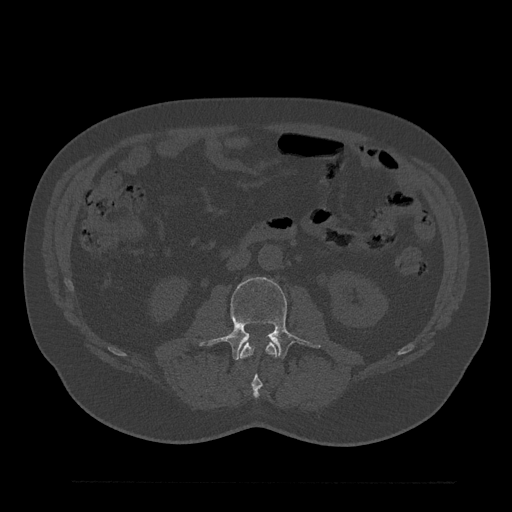
CT including the spine, one axial slice. Slice 54 of 797 in the series (ordered by position). Bone window (W 1800 / L 400 HU). 0.5 mm slice thickness. 512 × 512 image matrix, field of view 430 × 430 mm. Male patient, age 61 years. From the clinical record (not read from this slice): primary cancer: prostate.
Structures marked on this image (semi-automatic segmentation, software-assisted and operator-edited):
- L2 vertebra: bounding box [x1, y1, x2, y2] px = [239, 342, 278, 398]
- L3 vertebra: [203, 277, 320, 360]